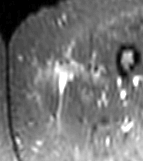
MRI of an extremity soft-tissue mass, one axial slice; slice 1 of 81 in the series (ordered by position); STIR; MR volume resampled by the dataset authors to the PET/CT grid (not the native acquisition matrix); 3.27 mm slice thickness; 143 × 161 image matrix. Female patient. Case-level facts recorded for this patient, not image findings: histological type: myxofibrosarcoma; grade: intermediate; site of the primary tumour: left thigh.
Structures marked on this image (expert contour drawn on MRI and transferred to this co-registered scan by the dataset authors):
- gross tumour volume including surrounding oedema: bounding box (x1, y1, x2, y2) in pixels: (53, 67, 102, 86)